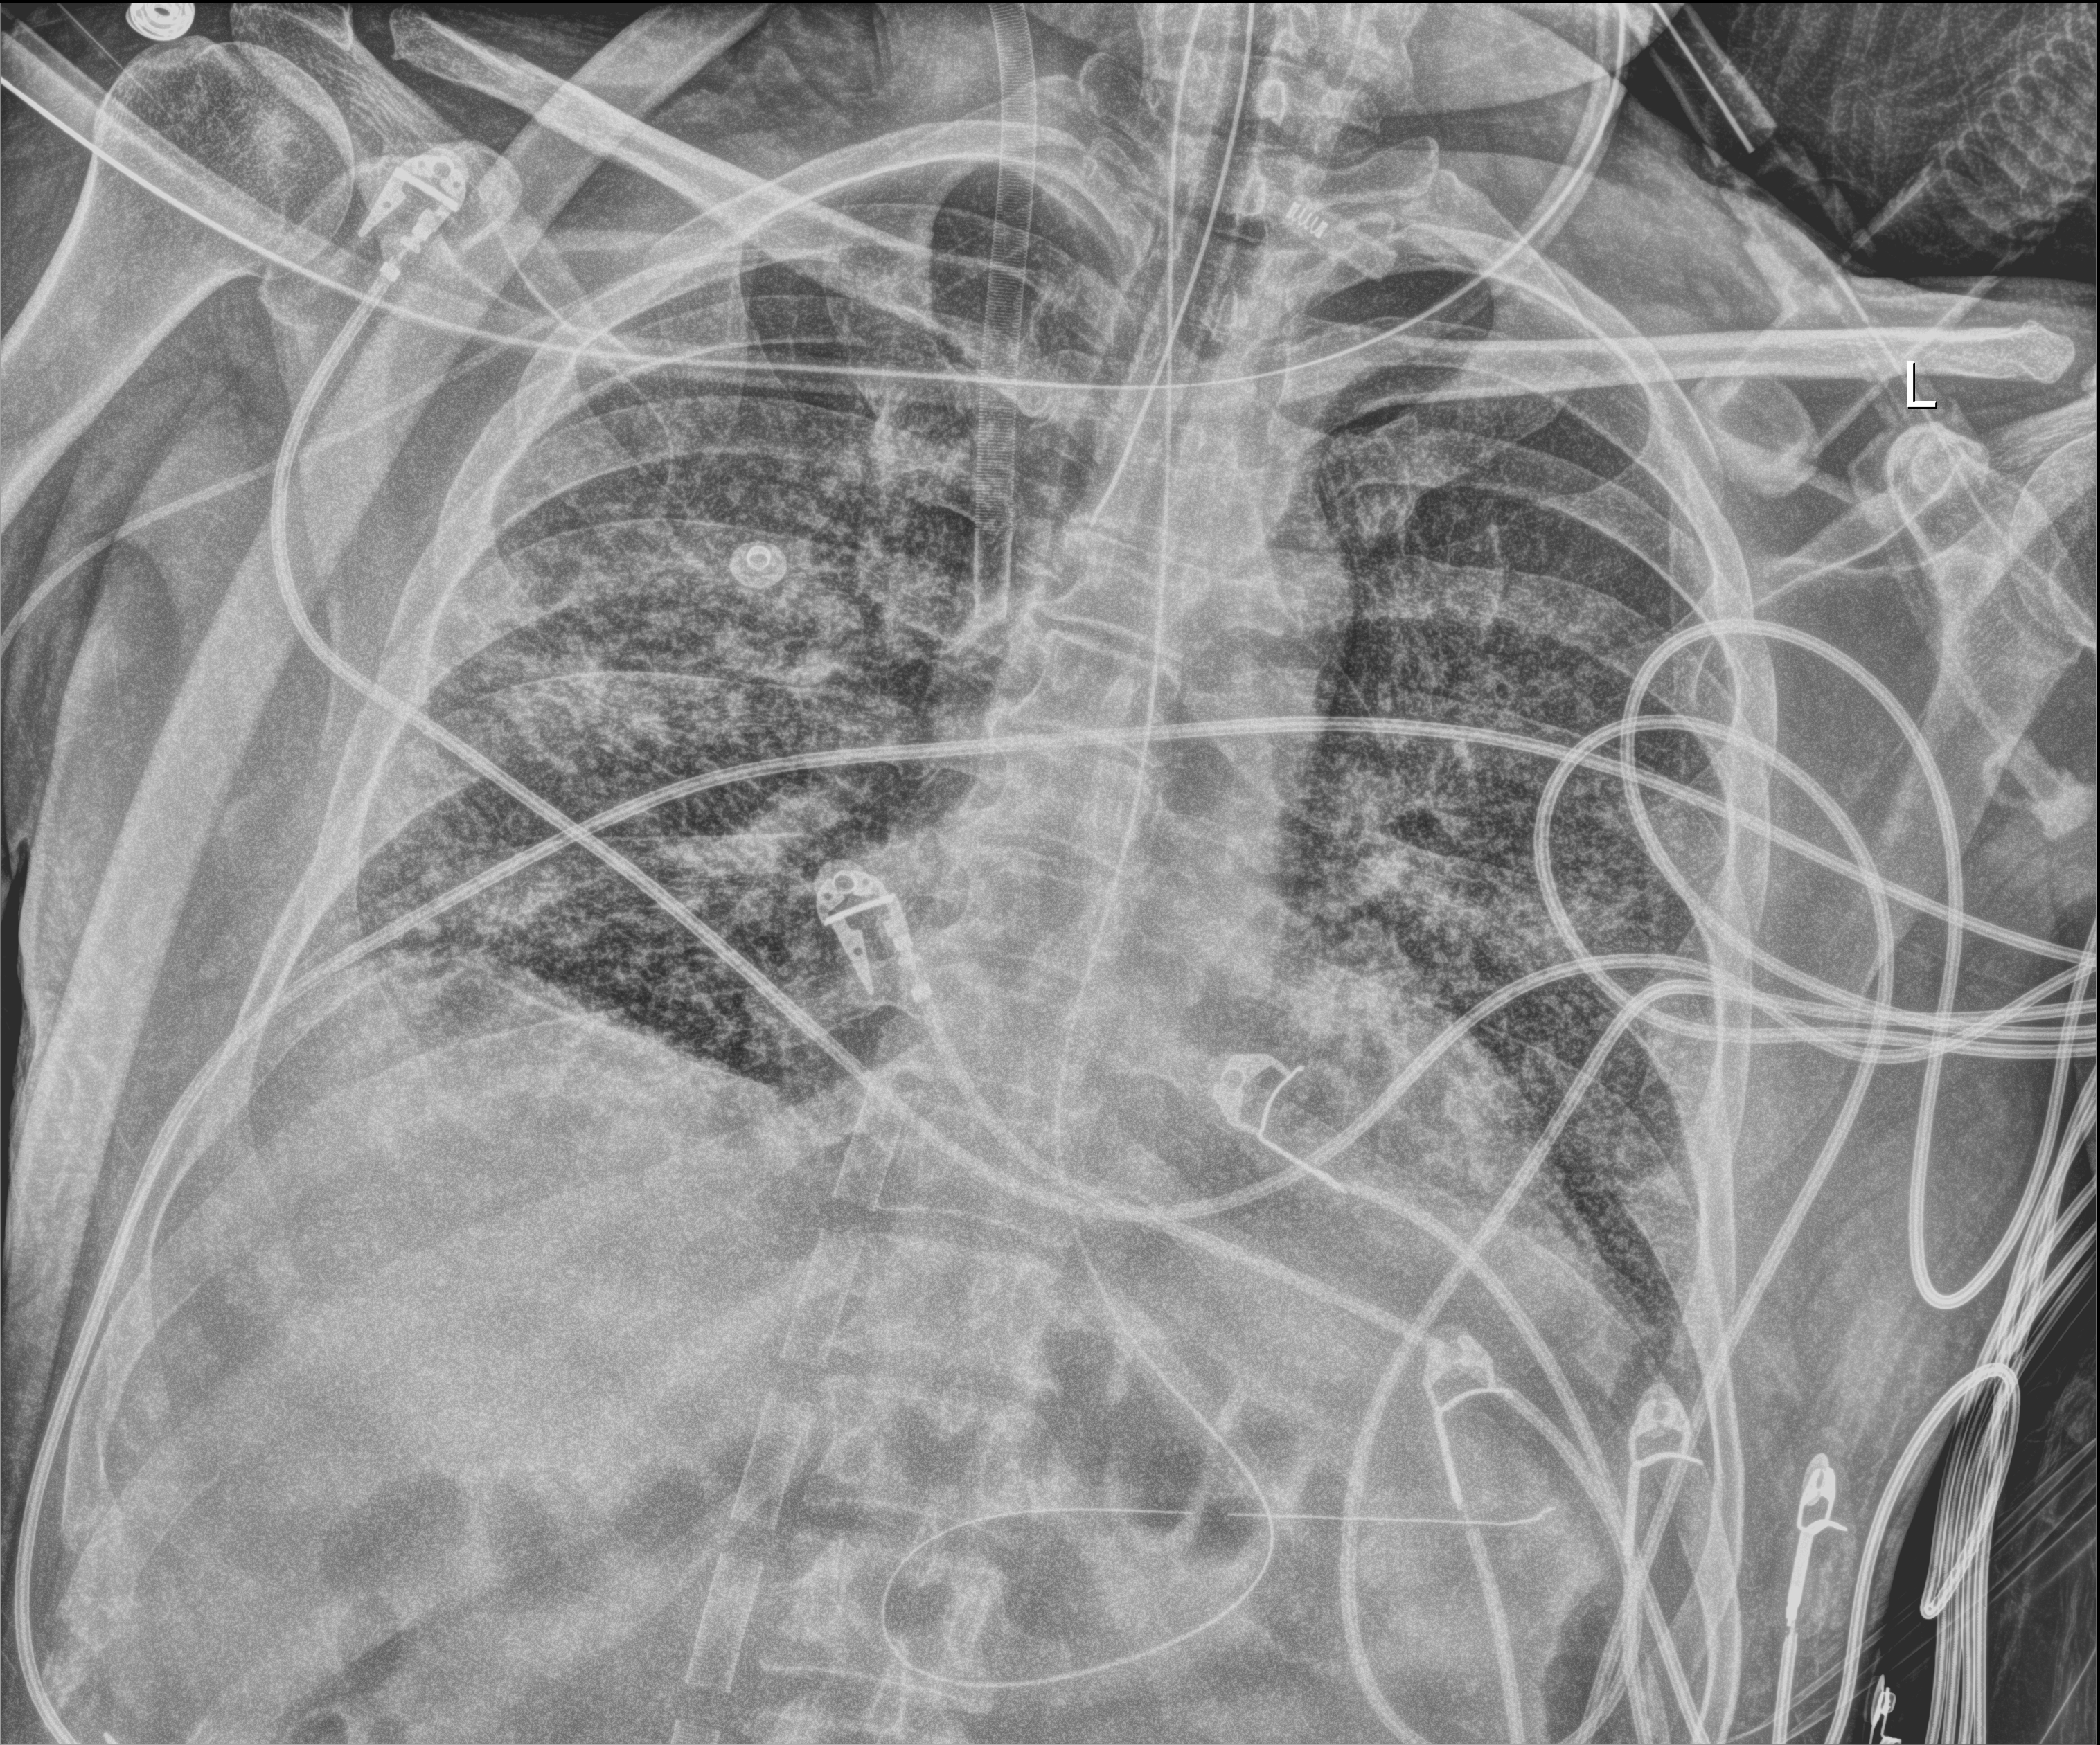
Chest X-ray (portable); anteroposterior (AP) projection. Patient hospitalised with COVID-19; male, aged 18–59 years.
Hospital-stay facts (about this admission, not read from this image; timing relative to this image not recorded): other chronic lung disease (admission record): no.